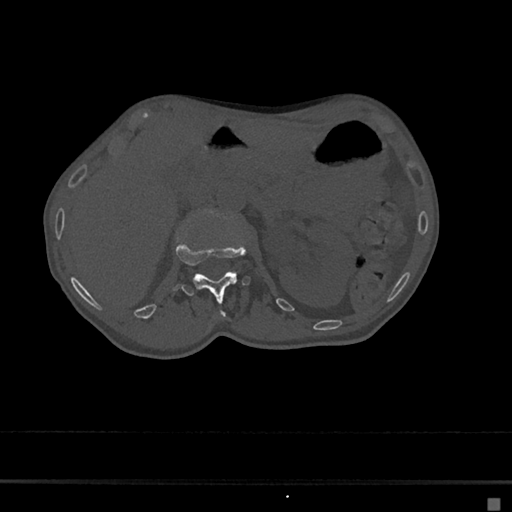
CT including the spine, one axial slice; position 64 of 797 along the scan axis; 120 kVp; bone window (W 1800 / L 400 HU); 0.5 mm slice thickness; 512 × 512 image matrix, field of view 360 × 360 mm. Patient: female, 68 years. Case-level facts recorded for this patient, not image findings: primary cancer: renal.
Annotated regions visible in this slice (semi-automatic segmentation, software-assisted and operator-edited):
- L1 vertebra: bounding box <172,239,252,301> (left, top, right, bottom; pixels)